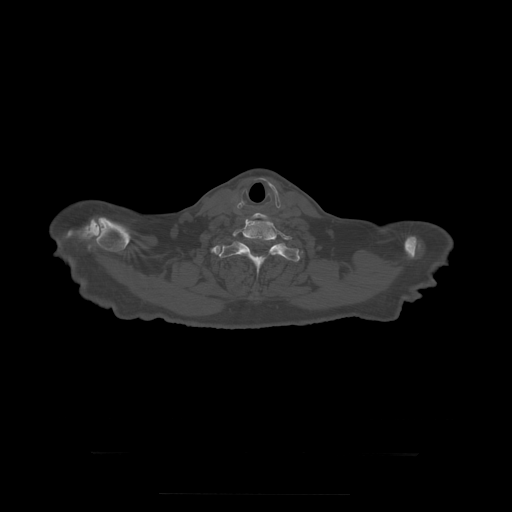
CT including the spine, one axial slice. Position 293 of 397 along the scan axis. Reconstruction kernel STANDARD. 120 kVp. Bone window (W 1800 / L 400 HU). 1.25 mm slice thickness. 512 × 512 image matrix. Patient age 73 years. From the clinical record (not read from this slice): primary cancer: prostate.
Annotated regions visible in this slice (semi-automatic segmentation, software-assisted and operator-edited):
- T1 vertebra: bounding box [x1, y1, x2, y2] px = [218, 241, 300, 279]